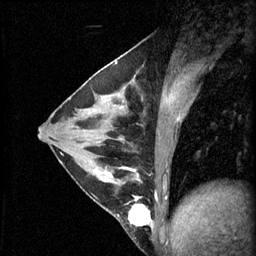
Breast MRI (dynamic contrast-enhanced), one sagittal slice. Position 26 of 60 along the scan axis. 3 images stored at this slice position (order not interpretable as contrast timing). 1.5 T. TE 4.2 ms, TR 11 ms. 256 × 256 image matrix. Female patient, age 29 years.
Outlined on this slice (semi-automatic segmentation, software-assisted and operator-edited):
- analysis volume of interest (the breast-tissue region the enhancement analysis was run in; not a lesion): bounding box <93,164,153,229> (left, top, right, bottom; pixels)
- tumour enhancement mask (voxels above the 70 % enhancement threshold inside the analysis volume of interest): <95,168,153,229>